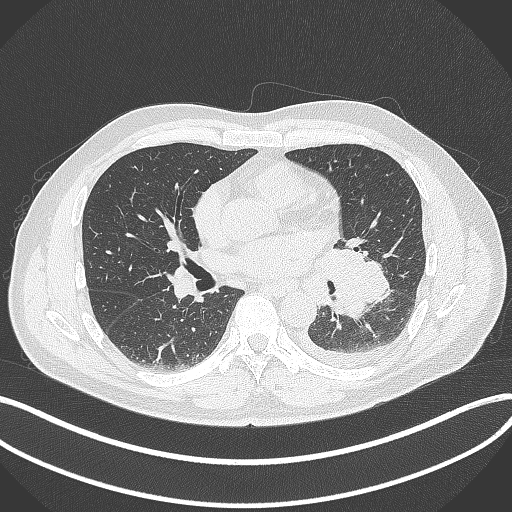
Chest CT, one axial slice; slice 181 of 342 in the series (ordered by position); 120 kVp; lung window (W 1500 / L -600 HU); 1 mm slice thickness; 512 × 512 image matrix. Patient: male, 58 years. From the clinical record (not read from this slice): clinical TNM (as recorded): T3 N1 M1b.
Structures marked on this image (bounding box drawn by a radiologist):
- lung tumour (recorded histology: small cell carcinoma): bounding box [x1, y1, x2, y2] px = [315, 236, 388, 321]